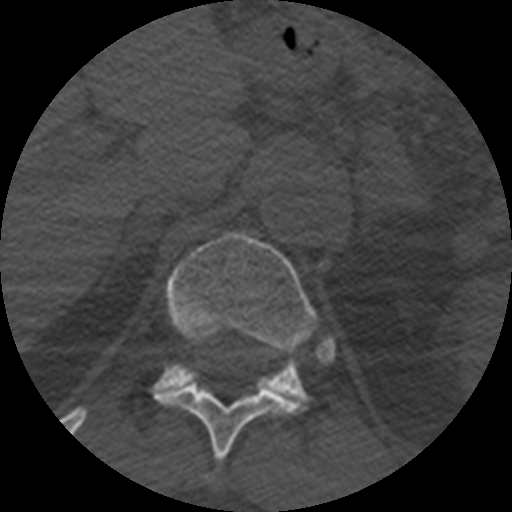
CT including the spine, one axial slice; slice 399 of 399 in the series (ordered by position); reconstruction kernel STANDARD; 120 kVp; bone window (W 1800 / L 400 HU); 1.25 mm slice thickness; 512 × 512 image matrix. Patient age 71 years. Case-level facts recorded for this patient, not image findings: primary cancer: prostate.
Outlined on this slice (semi-automatically segmented with operator editing):
- T11 vertebra: bounding box <157,386,302,484> (left, top, right, bottom; pixels)
- T12 vertebra: <153,232,337,406>